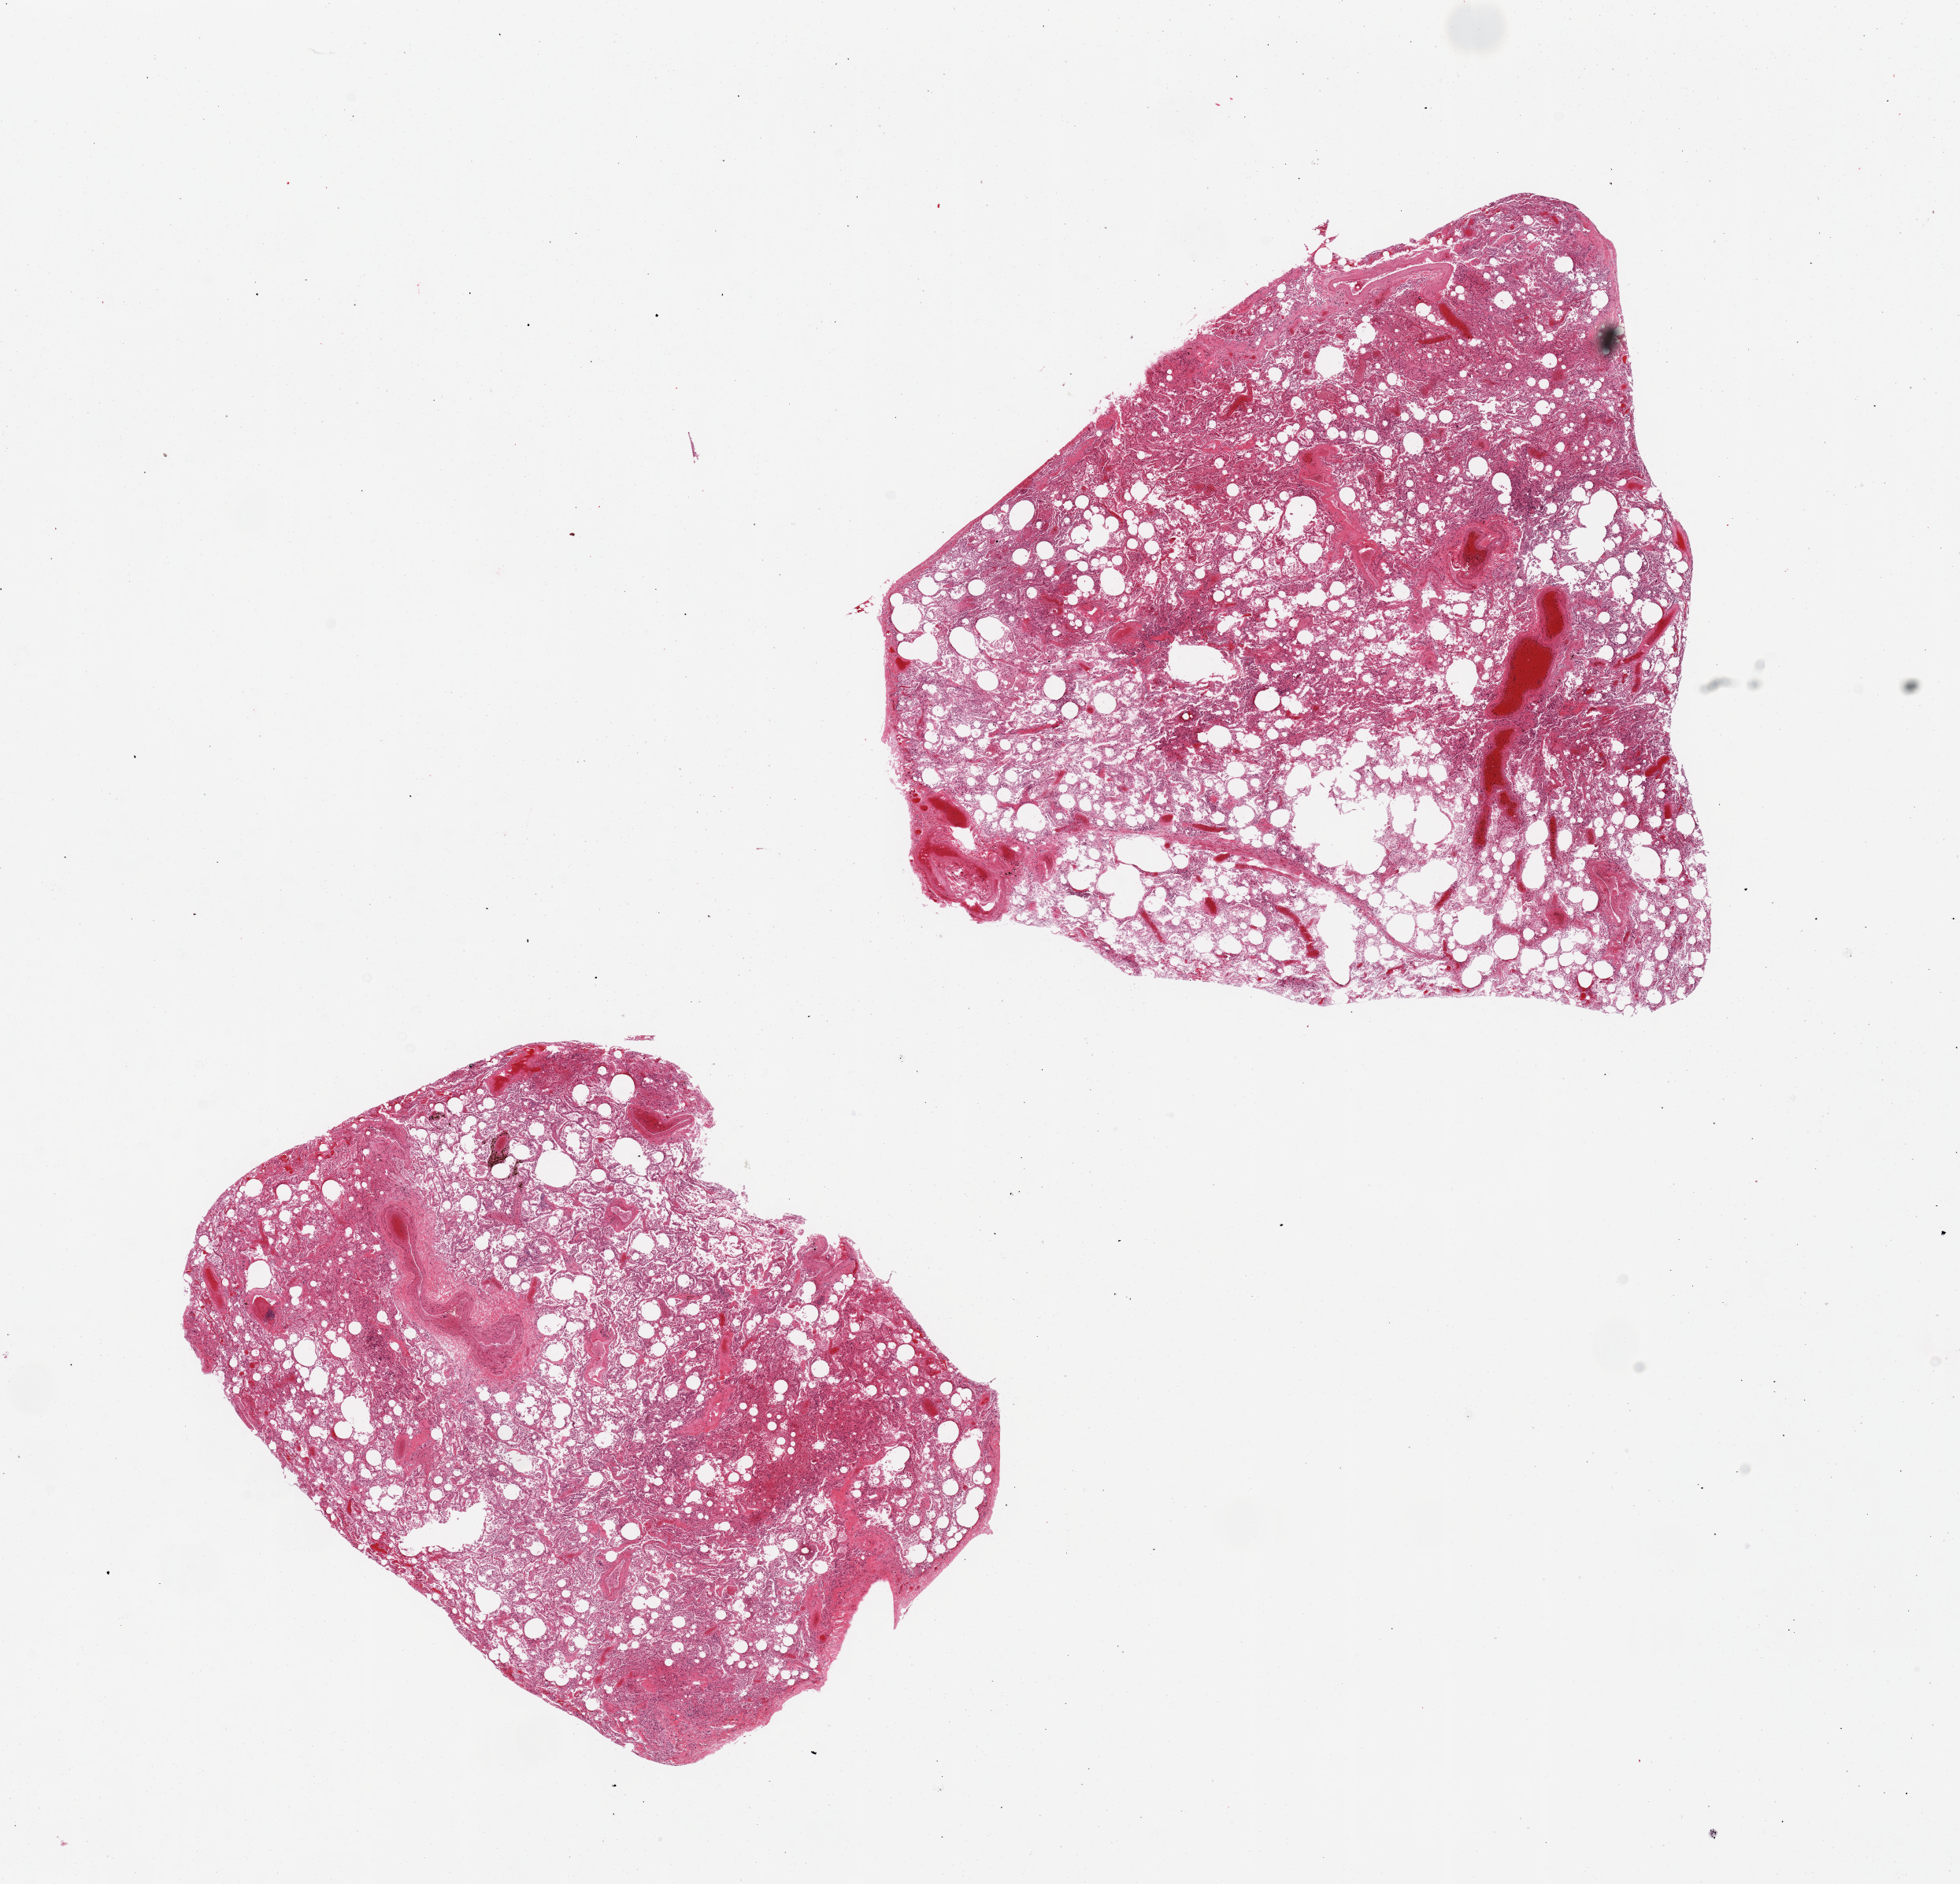
Digitized hematoxylin and eosin (H&E)-stained section — shown as a low-resolution overview of the whole scanned area (about 19.7 x 18.9 mm, acquisition: 20x scan). PAXgene-fixed, paraffin-embedded tissue. Target tissue: lung. Donor tissue sample. Donor: female.
• reviewer comment on this tissue sample: 2 pieces, hemosiderin-laden macrophages, congestion